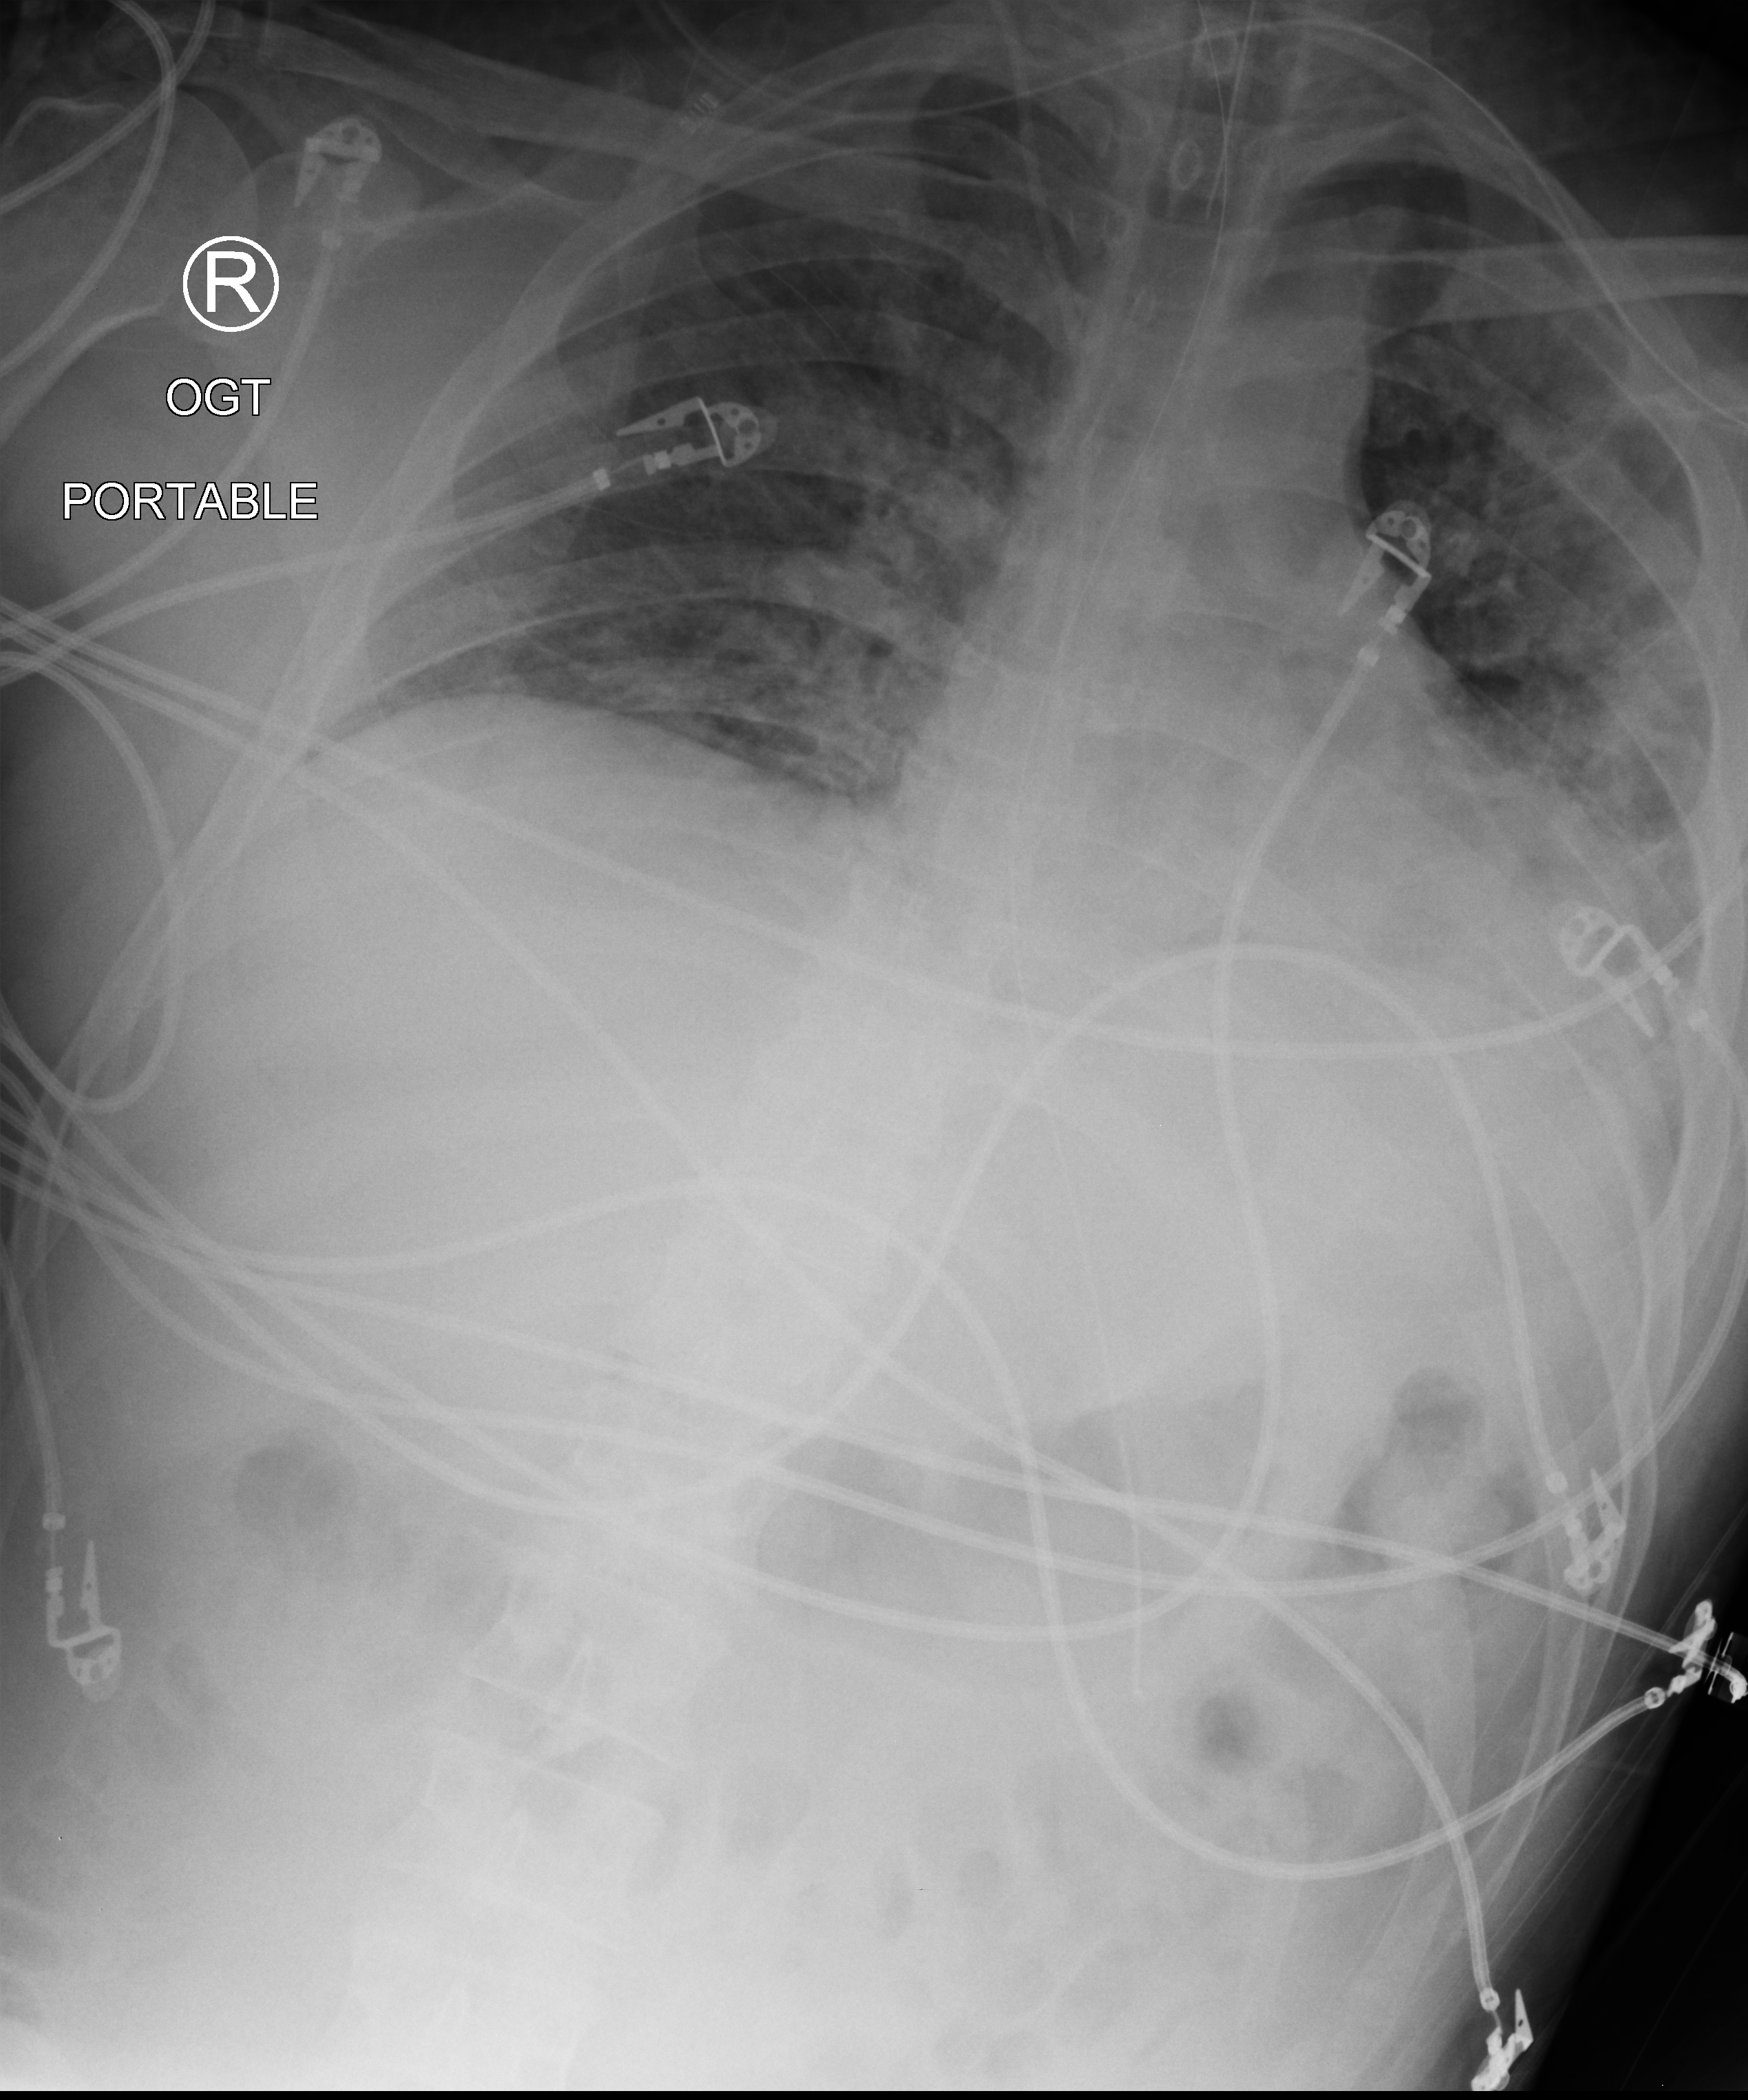
Bedside chest radiograph (computed radiography); anteroposterior (AP) projection. Patient hospitalised with COVID-19; male, aged 18–59 years.
Admission-level facts for this patient (not findings on this image; timing relative to this image not recorded): admitted to intensive care during this hospital stay: yes; mechanically ventilated during this hospital stay: yes.